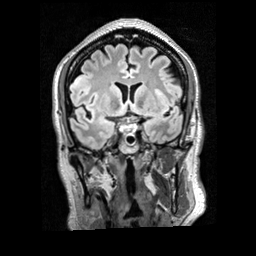
Brain MRI from a brain-tumour surgery series, one coronal slice. Position 119 of 200 along the scan axis. T2 FLAIR. 1 mm slice thickness. 256 × 256 image matrix, field of view 256 × 256 mm. From the clinical record (not read from this slice): histopathology: Glioblastoma; WHO grade: 4; IDH mutation: no; tumour location: Right Frontal.
Outlined on this slice (expert manual segmentation):
- tumour: box from (x=69, y=73) to (x=92, y=89) px